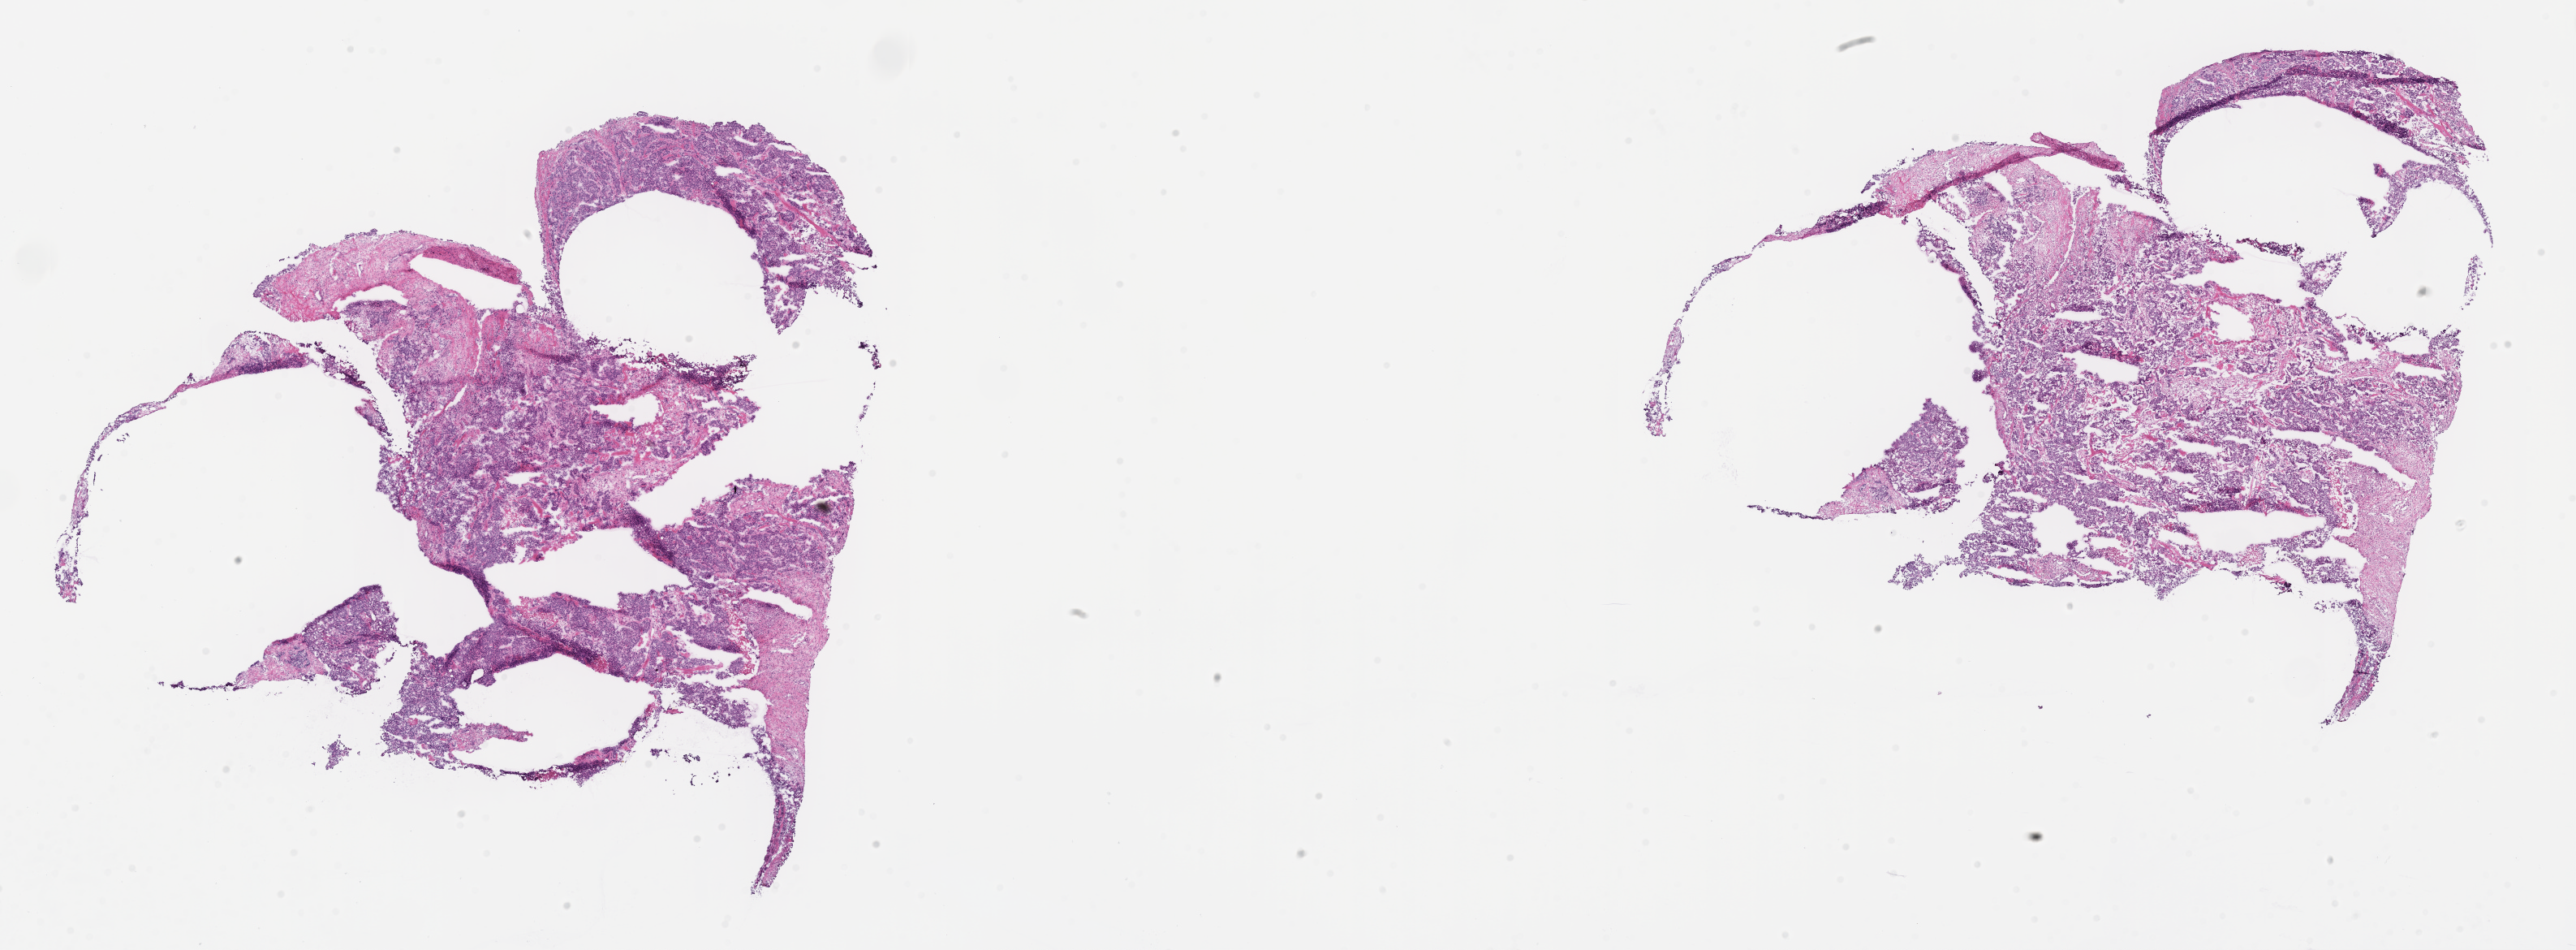
H&E whole-slide image — a low-resolution overview of the entire scanned area, about 25.6 x 9.4 mm, cryosection, specimen: primary tumor, site: breast (left). Patient: female, age at initial diagnosis 55 years. Slide review estimates, as recorded: tumor cells 70%, tumor nuclei 70%, stromal cells 20%, necrosis 0%, normal cells 10%. Inflammatory infiltration, as recorded: lymphocyte infiltration 5%, monocyte infiltration 0%, neutrophil infiltration 0%.
- histologic diagnosis: Infiltrating duct carcinoma, NOS
- section: bottom of the tissue portion